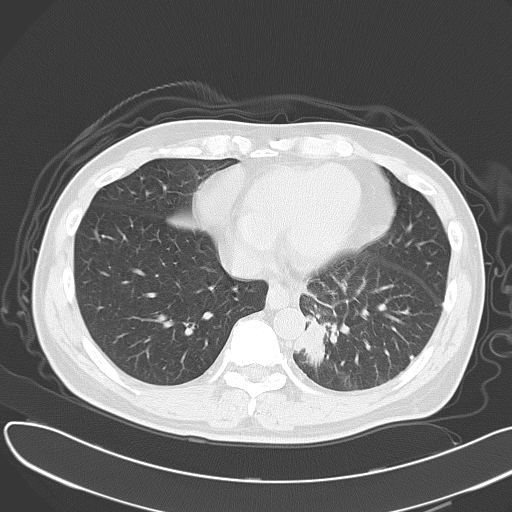
Chest CT, one axial slice. Lung window (W 1500 / L -600 HU). 5 mm slice thickness. 512 × 512 image matrix, field of view 376 × 376 mm. Male patient, age 55 years. From the clinical record (not read from this slice): clinical TNM (as recorded): T2 N3 M0.
Annotated regions visible in this slice (bounding box drawn by a radiologist):
- lung tumour (recorded histology: small cell carcinoma): bounding box [x1, y1, x2, y2] px = [293, 312, 339, 377]